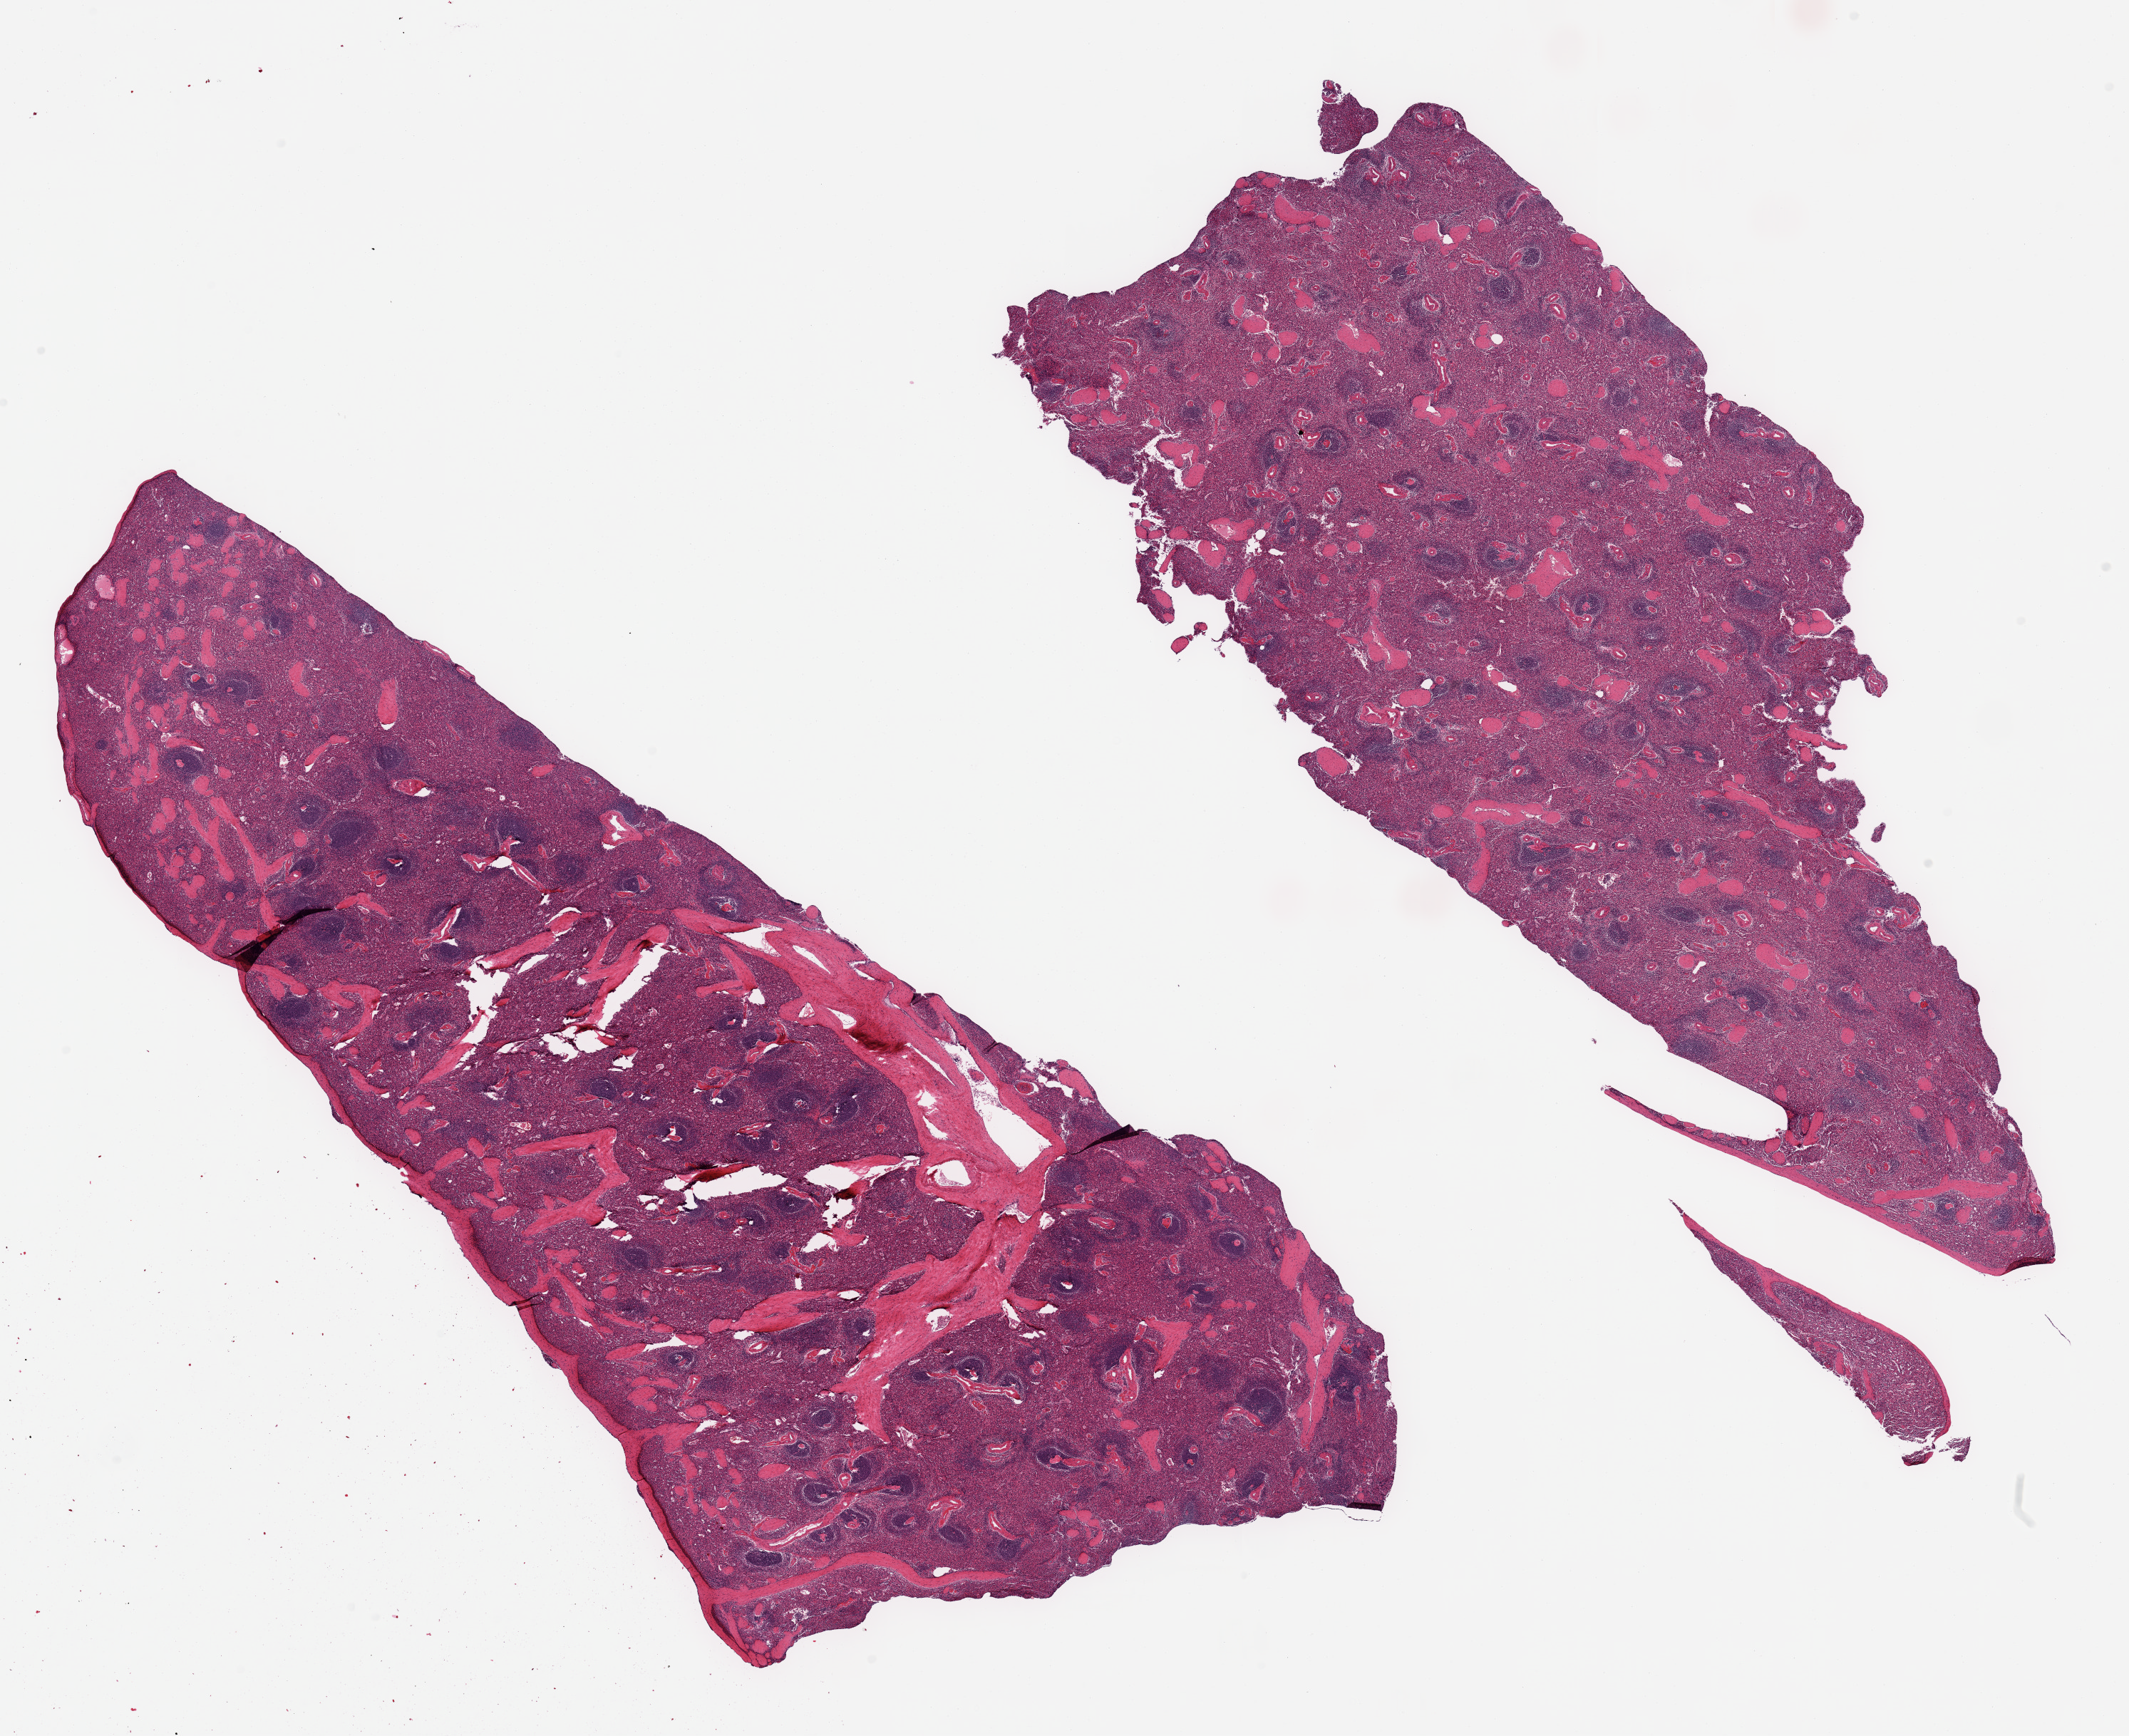
Digitized hematoxylin and eosin (H&E)-stained section — a low-resolution overview of the entire scanned area, about 23.6 x 19.3 mm, PAXgene-fixed paraffin-embedded (PFPE) section, section of spleen (target tissue), tissue donor sample. Donor: female.
Review note (as recorded): 2 pieces, no abnormality.